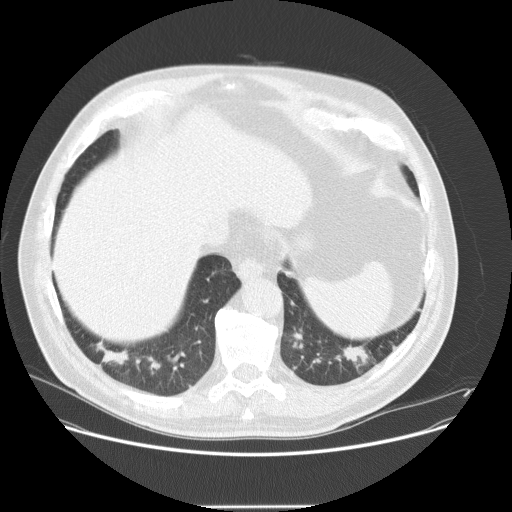
Low-dose screening chest CT, axial slice. Baseline screening round. Lung window (W 1500 / L -600 HU). Standard (soft-tissue) reconstruction kernel (STANDARD). 120 kVp. Male, age 61 years at enrolment. Current smoker at enrolment.
Lesion marked by an expert reader, bounding box <90,335,144,386> (left, top, right, bottom; pixels). The screening reader recorded 2 non-calcified nodules or masses ≥4 mm on this exam (left lower lobe, right lower lobe); which of them this box marks is not recorded. Official screen result: positive, change unspecified: nodule(s) >= 4 mm or enlarging nodule(s), mass(es), or other non-specific abnormalities suspicious for lung cancer.